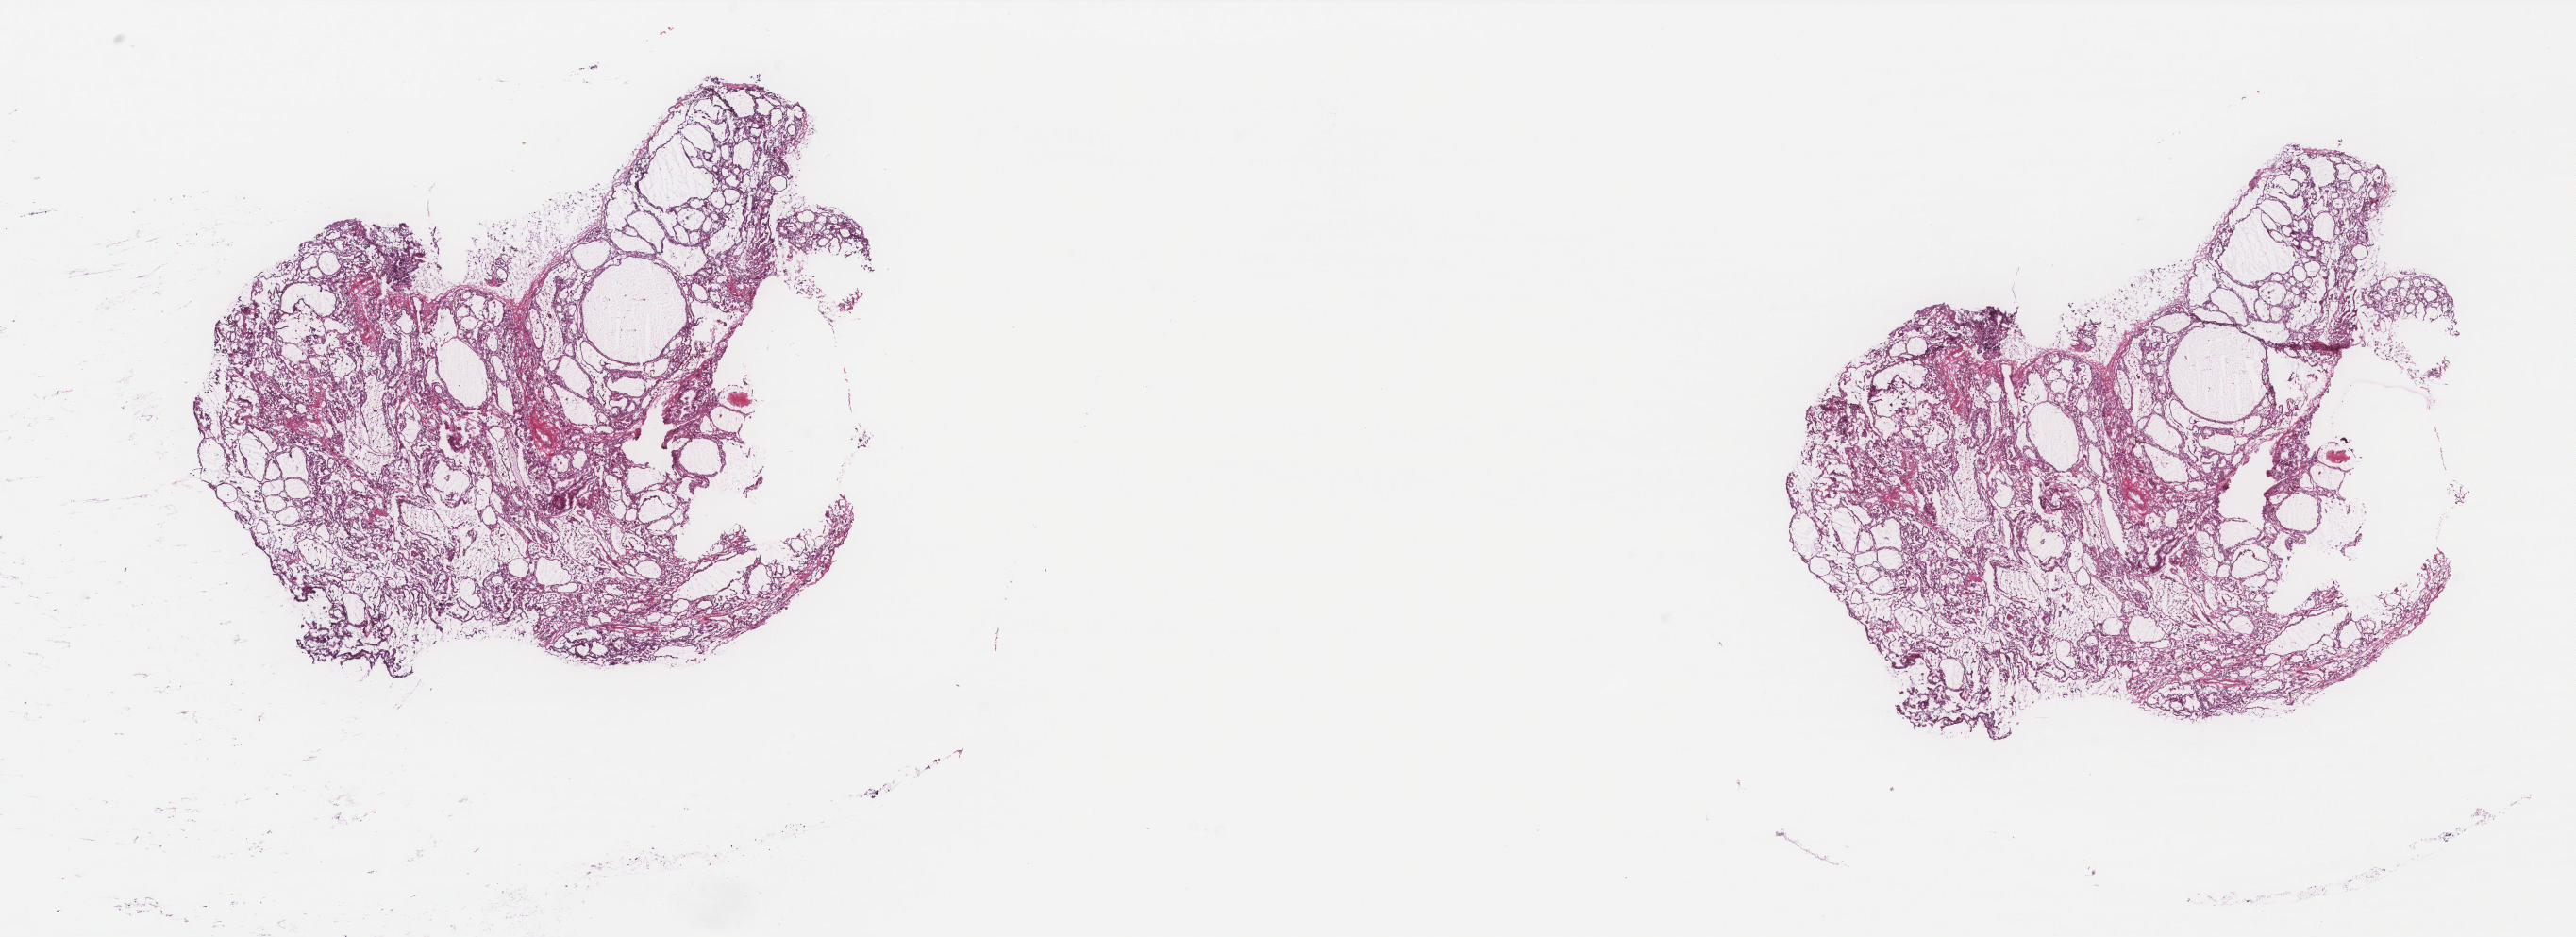
Hematoxylin and eosin (H&E) stained whole-slide image, a low-resolution overview of the entire scanned area, about 21.9 x 8.0 mm (from a 40x scan), frozen section from the top of the tissue portion, thyroid, primary tumour sample. Patient: female, age at initial diagnosis 39 years. Composition of this section per pathologist review: tumour cells 100%, tumour nuclei 75%, normal cells 0%, stromal cells 0%, necrosis 0%. Infiltration values recorded for this section: lymphocyte infiltration 0%, monocyte infiltration 0%, neutrophil infiltration 0%.
Pathologic diagnosis: Papillary carcinoma, follicular variant (thyroid gland). AJCC pathologic stage: I.